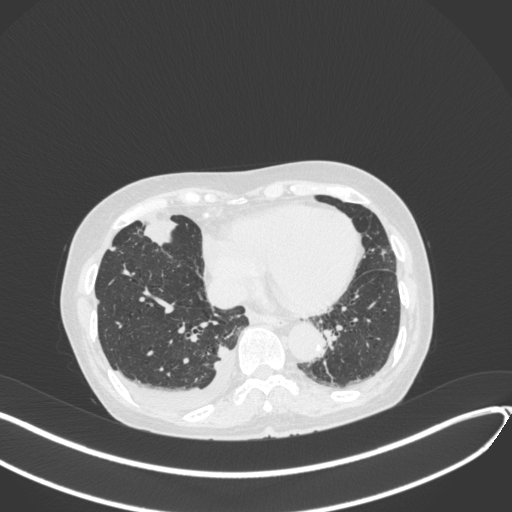
Chest CT, one axial slice; slice 119 of 418 in the series (ordered by position); lung window (W 1500 / L -600 HU); 1 mm slice thickness; 512 × 512 image matrix, field of view 400 × 400 mm. Female patient, age 75 years. From the clinical record (not read from this slice): clinical TNM (as recorded): T2a N3 M0.
Annotated regions visible in this slice (rectangle marked by the reading radiologist):
- lung tumour (recorded histology: adenocarcinoma): bounding box <144,218,178,246> (left, top, right, bottom; pixels)